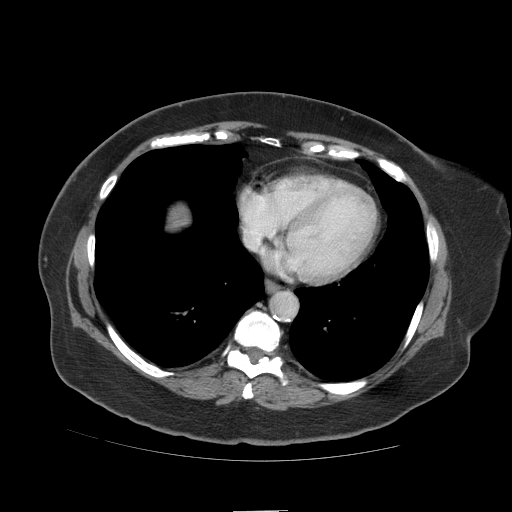
Contrast-enhanced abdominal CT (liver protocol), one axial slice. Slice 104 of 109 in the series (ordered by position). 140 kVp. Soft-tissue window (W 400 / L 40 HU). 512 × 512 image matrix. From the clinical record (not read from this slice): diagnosis: hepatocellular carcinoma (patient treated with transarterial chemoembolisation; whether this scan precedes or follows treatment is not stated here); TNM stage (as recorded): Stage-IVB; Child-Pugh class: A.
Outlined on this slice (semi-automatic segmentation, software-assisted and operator-edited):
- liver parenchyma outside the tumour (the mass and vessels are separate outlines, so this box may not span the whole liver): bounding box (x1, y1, x2, y2) in pixels: (170, 206, 188, 228)